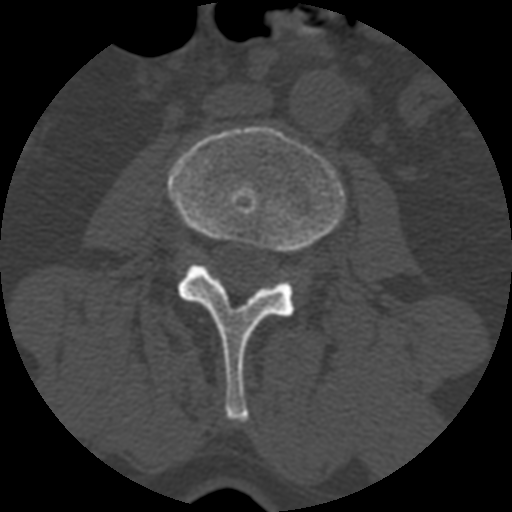
CT including the spine, one axial slice; position 302 of 399 along the scan axis; reconstruction kernel STANDARD; bone window (W 1800 / L 400 HU); 1.25 mm slice thickness; 512 × 512 image matrix, field of view 160 × 160 mm. Patient age 71 years. Case-level facts recorded for this patient, not image findings: primary cancer: prostate.
Structures marked on this image (semi-automatic segmentation, software-assisted and operator-edited):
- L3 vertebra: bounding box (x1, y1, x2, y2) in pixels: (168, 127, 345, 421)